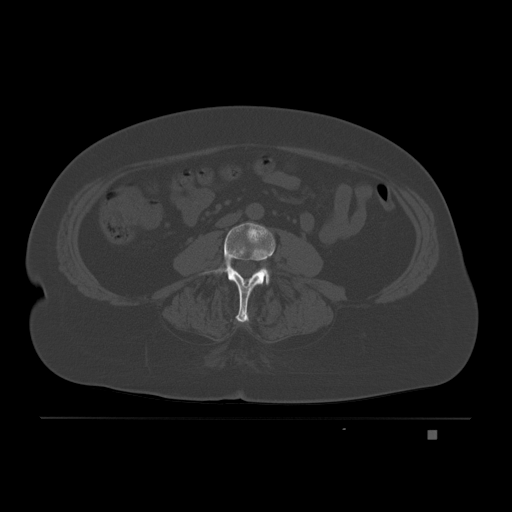
CT including the spine, one axial slice. Slice 49 of 221 in the series (ordered by position). Bone window (W 1800 / L 400 HU). 3 mm slice thickness. 512 × 512 image matrix, field of view 474 × 474 mm. Female patient, age 63 years. From the clinical record (not read from this slice): primary cancer: breast.
Outlined on this slice (semi-automatic segmentation, software-assisted and operator-edited):
- L3 vertebra: bounding box <202,222,276,322> (left, top, right, bottom; pixels)
- L4 vertebra: <265,271,270,284>